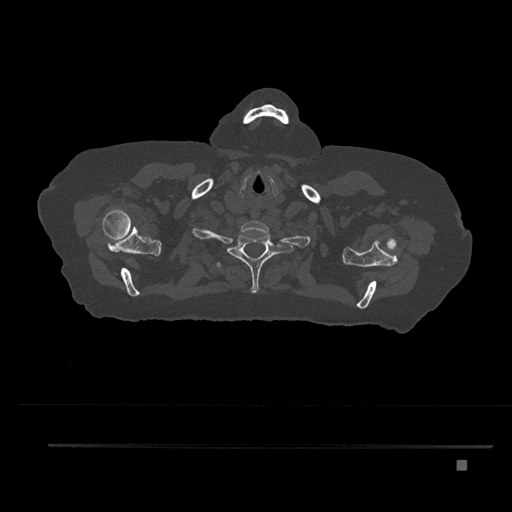
CT including the spine, one axial slice. Position 700 of 797 along the scan axis. 120 kVp. Bone window (W 1800 / L 400 HU). 0.5 mm slice thickness. 512 × 512 image matrix, field of view 437 × 437 mm. Female patient, age 76 years. Case-level facts recorded for this patient, not image findings: primary cancer: lung; vertebrae with lytic lesions (as recorded): T11, L3.
Annotated regions visible in this slice (semi-automatically segmented with operator editing):
- T1 vertebra: box from (x=227, y=232) to (x=283, y=293) px
- T2 vertebra: (x=217, y=247)–(x=234, y=268)